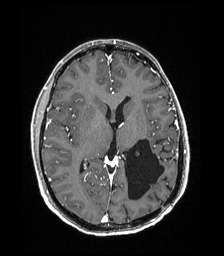
Brain MRI from a brain-tumour surgery series, one axial slice. Position 94 of 192 along the scan axis. T1-weighted post-contrast. 1 mm slice thickness. 224 × 256 image matrix. From the clinical record (not read from this slice): histopathology: Low grade glioma; IDH mutation: no; tumour location: Left Parieto-Occipital Intraventricular.
Outlined on this slice (manually delineated by an expert):
- previous resection cavity: bounding box [x1, y1, x2, y2] px = [125, 139, 164, 200]
- tumour: [134, 150, 141, 157]